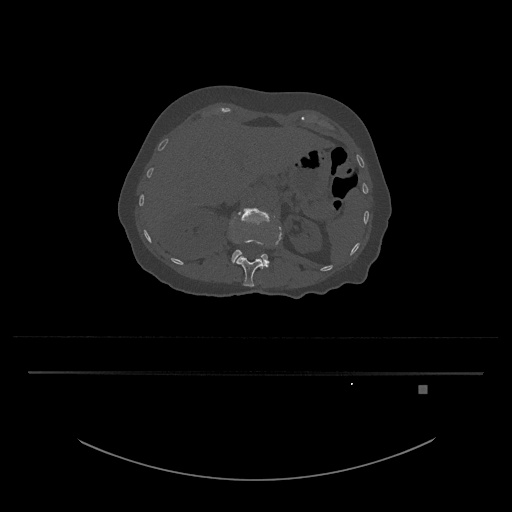
CT including the spine, one axial slice. Position 531 of 797 along the scan axis. Reconstruction kernel Br40s/3. 120 kVp. Bone window (W 1800 / L 400 HU). 0.5 mm slice thickness. 512 × 512 image matrix, field of view 500 × 500 mm. Female patient, age 57 years. Case-level facts recorded for this patient, not image findings: primary cancer: cervical.
Outlined on this slice (semi-automatic segmentation, software-assisted and operator-edited):
- L1 vertebra: bounding box [x1, y1, x2, y2] px = [232, 226, 282, 287]